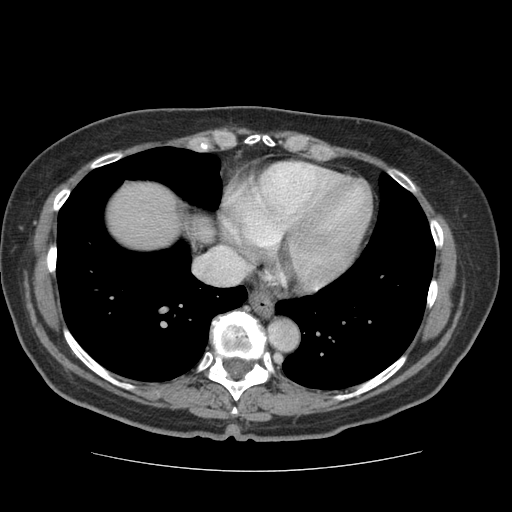
Contrast-enhanced abdominal CT (liver protocol), one axial slice; soft-tissue window (W 400 / L 40 HU); 2.5 mm slice thickness; 512 × 512 image matrix. From the clinical record (not read from this slice): diagnosis: hepatocellular carcinoma (patient treated with transarterial chemoembolisation; whether this scan precedes or follows treatment is not stated here); TNM stage (as recorded): Stage-I; Child-Pugh class: A; tumour differentiation: moderately differentiated.
Structures marked on this image (semi-automatically segmented with operator editing):
- liver parenchyma outside the tumour (the mass and vessels are separate outlines, so this box may not span the whole liver): bounding box [x1, y1, x2, y2] px = [108, 182, 180, 248]